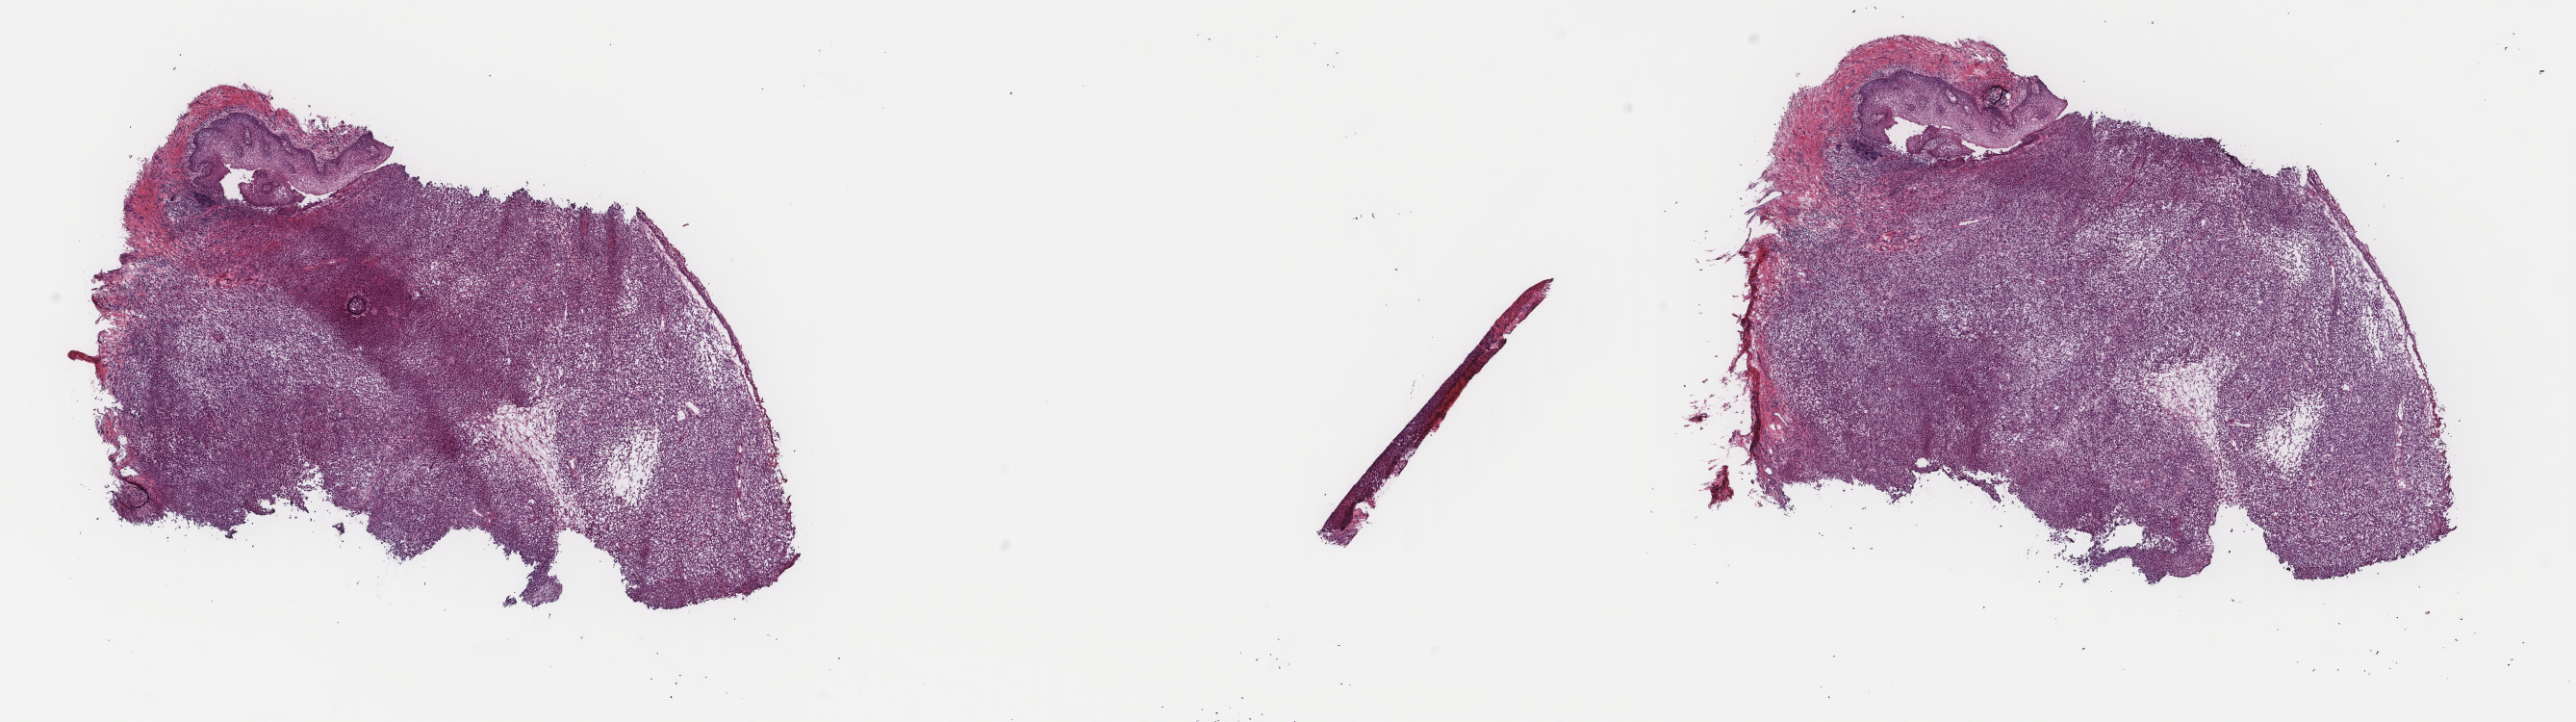
H&E-stained whole-slide image — low-resolution overview of the scanned area, about 21.2 x 6.0 mm (acquisition: 40x scan). Frozen section from the top of the tissue portion. Metastatic tumour sample, sampled site: vagina. Female patient; age at initial diagnosis 59 years. Slide review estimates, as recorded: tumour cells 95%, tumour nuclei 90%, normal cells 5%, stromal cells 0%, necrosis 0%. Infiltration values recorded for this section: lymphocyte infiltration 5%, monocyte infiltration 0%, neutrophil infiltration 0%.
• this section: metastatic tumour tissue
• patient diagnosis: Malignant melanoma, NOS